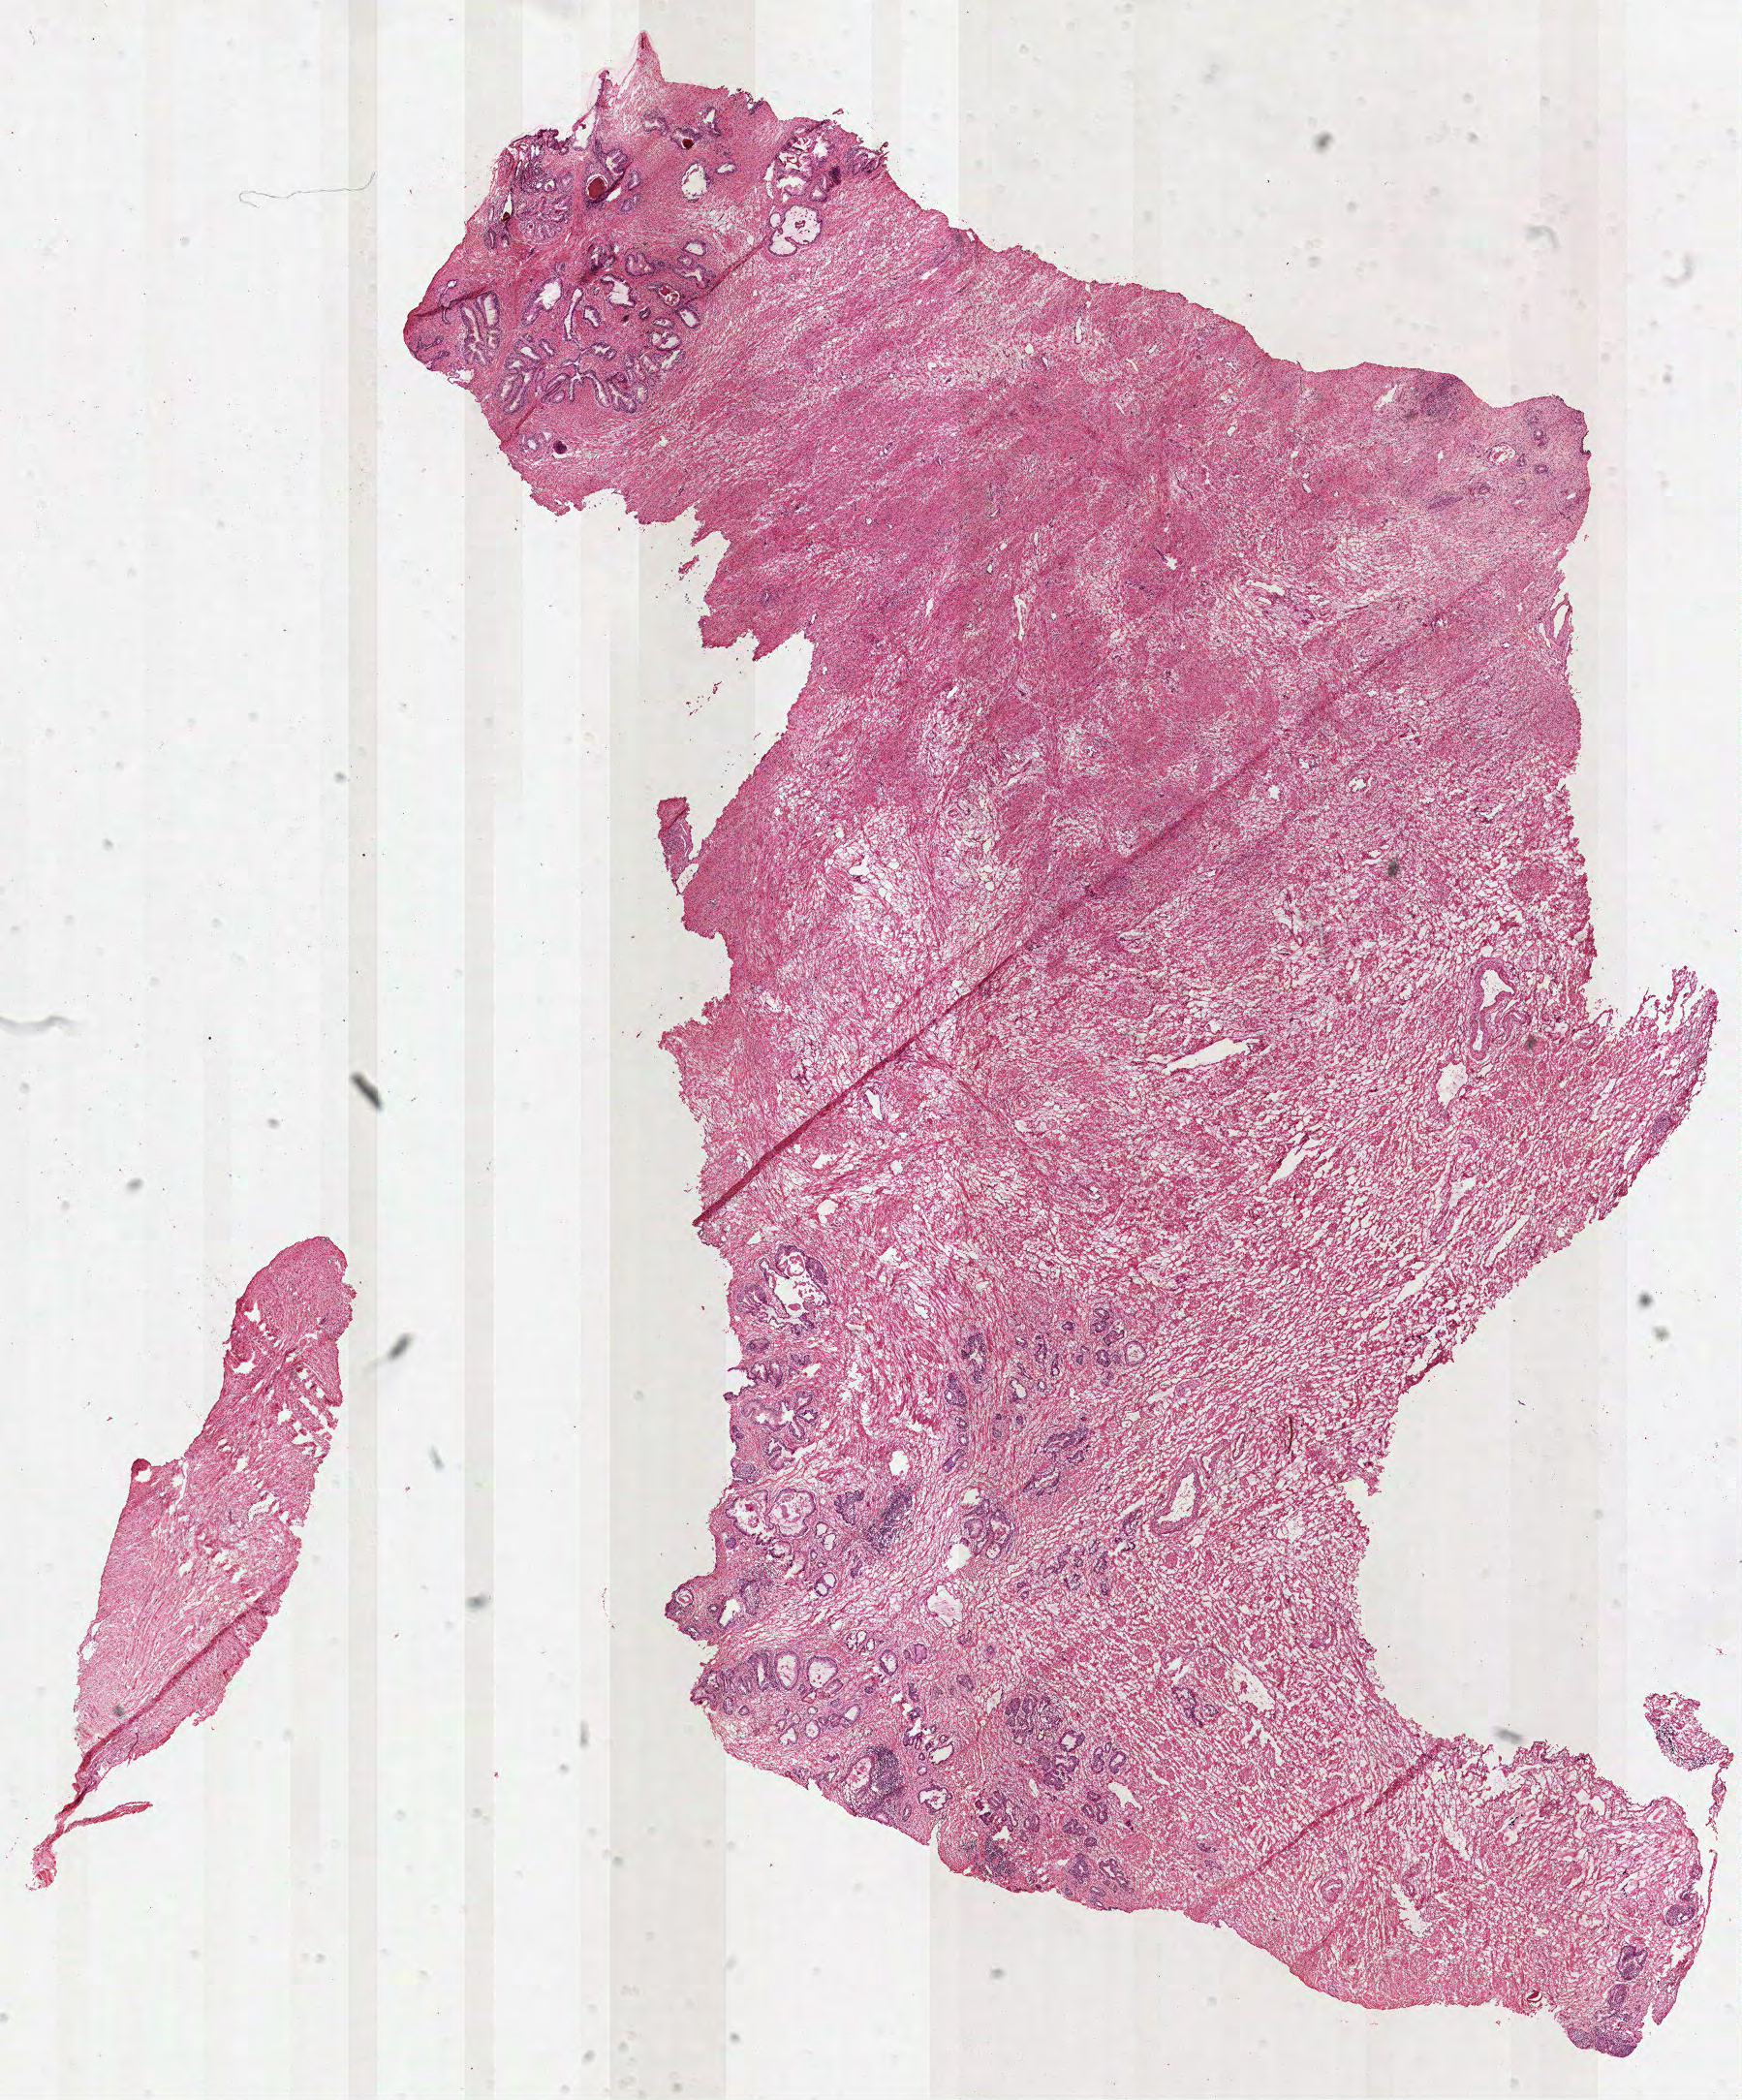
Digitized H&E tissue section (whole slide) — shown as a low-resolution overview of the whole scanned area (about 14.5 x 17.5 mm). Frozen section from the top of the tissue portion. Sample: solid tissue normal (non-tumour tissue), prostate. Male, age 63 years at initial diagnosis.
* this section: solid tissue normal sample (biorepository sample class)
* patient diagnosis: Acinar cell carcinoma (prostate gland)